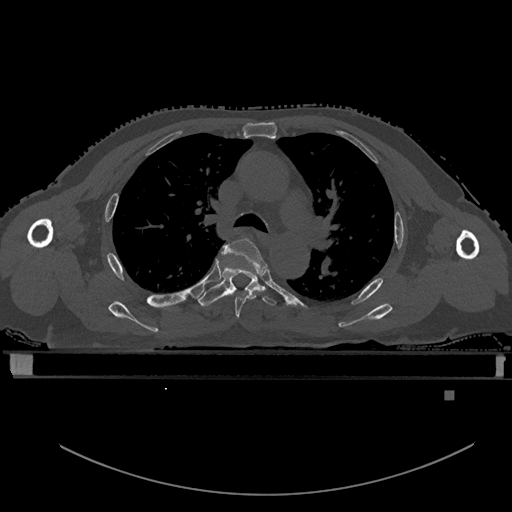
CT including the spine, one axial slice. Slice 380 of 969 in the series (ordered by position). Bone window (W 1800 / L 400 HU). 0.5 mm slice thickness. 512 × 512 image matrix, field of view 456 × 456 mm. Male patient, age 82 years. From the clinical record (not read from this slice): primary cancer: prostate; vertebrae with lytic lesions (as recorded): T11, T9, T8, T2.
Outlined on this slice (semi-automatic segmentation, software-assisted and operator-edited):
- T4 vertebra: bounding box (x1, y1, x2, y2) in pixels: (222, 238, 267, 318)
- T5 vertebra: (198, 255, 277, 307)